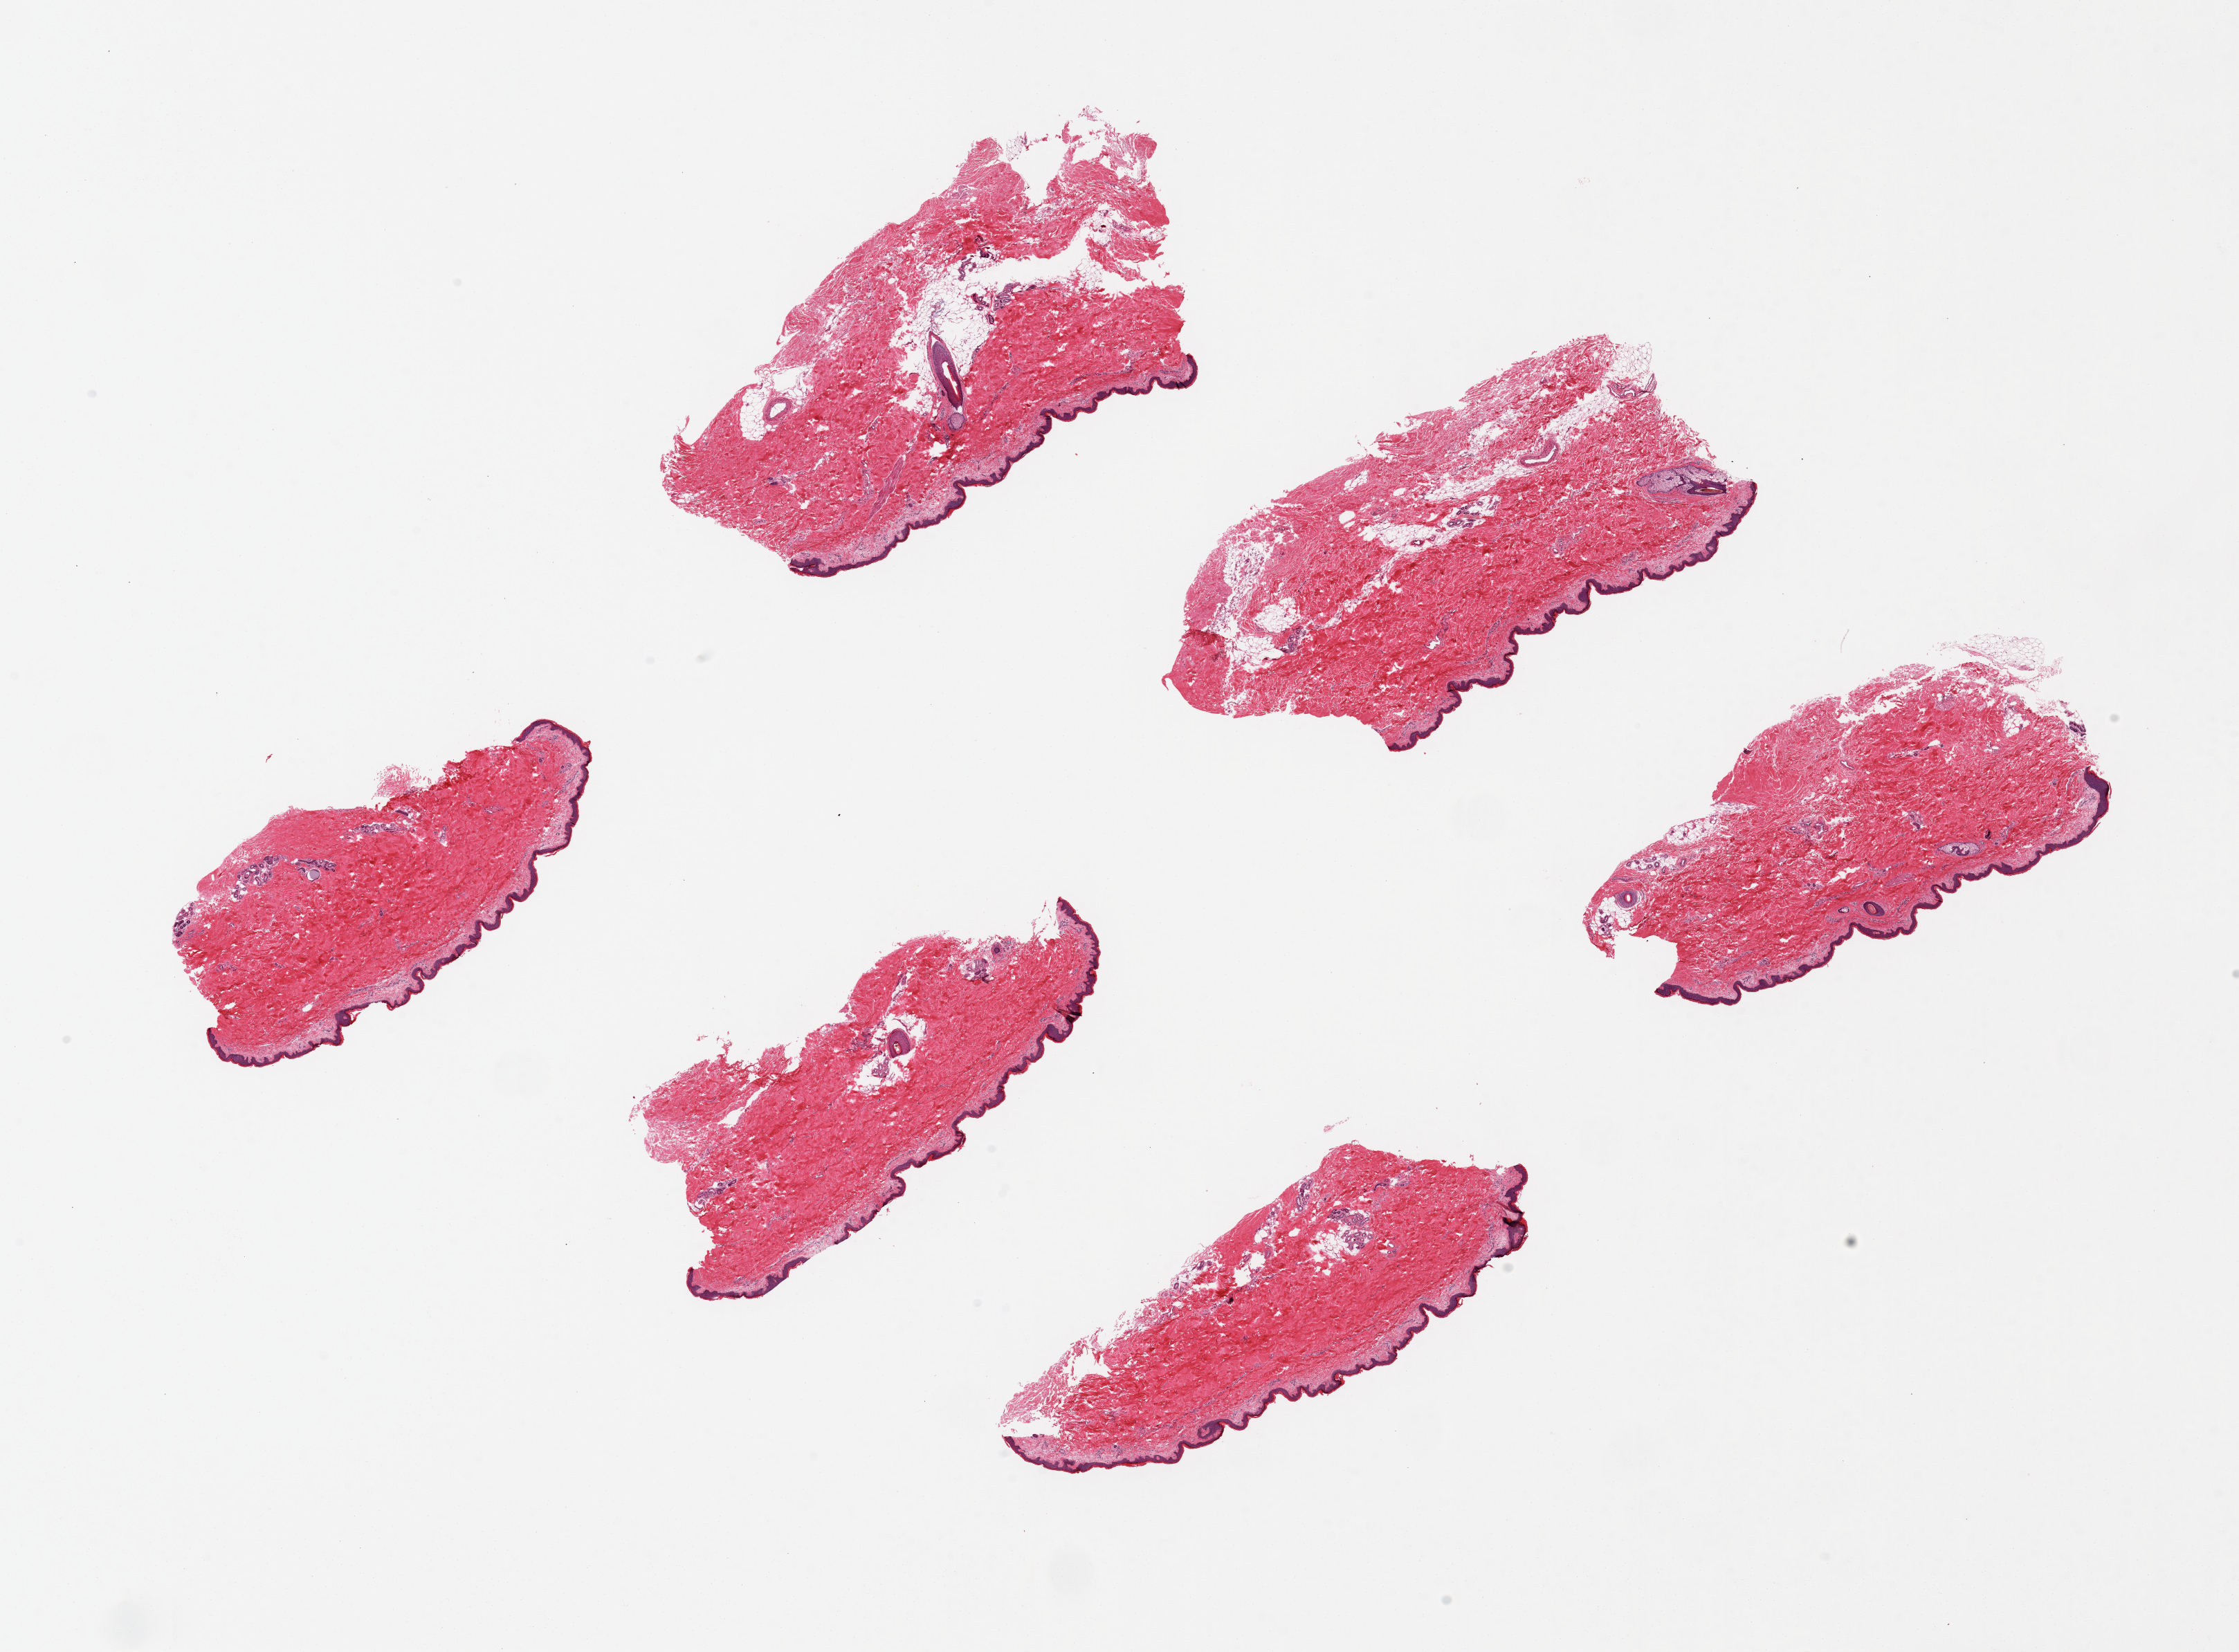
Whole-slide image, haematoxylin and eosin stain — a low-resolution overview of the entire scanned area, about 25.6 x 18.9 mm (acquisition: 20x scan). PAXgene-fixed, paraffin-embedded tissue. Sampled site (target tissue): skin of lower leg. Tissue donor sample. Donor sex: male.
• reviewer comment on this tissue sample: 6 pieces, ~6x2.5mm. Squamous epithelium is ~2-3% of thickness